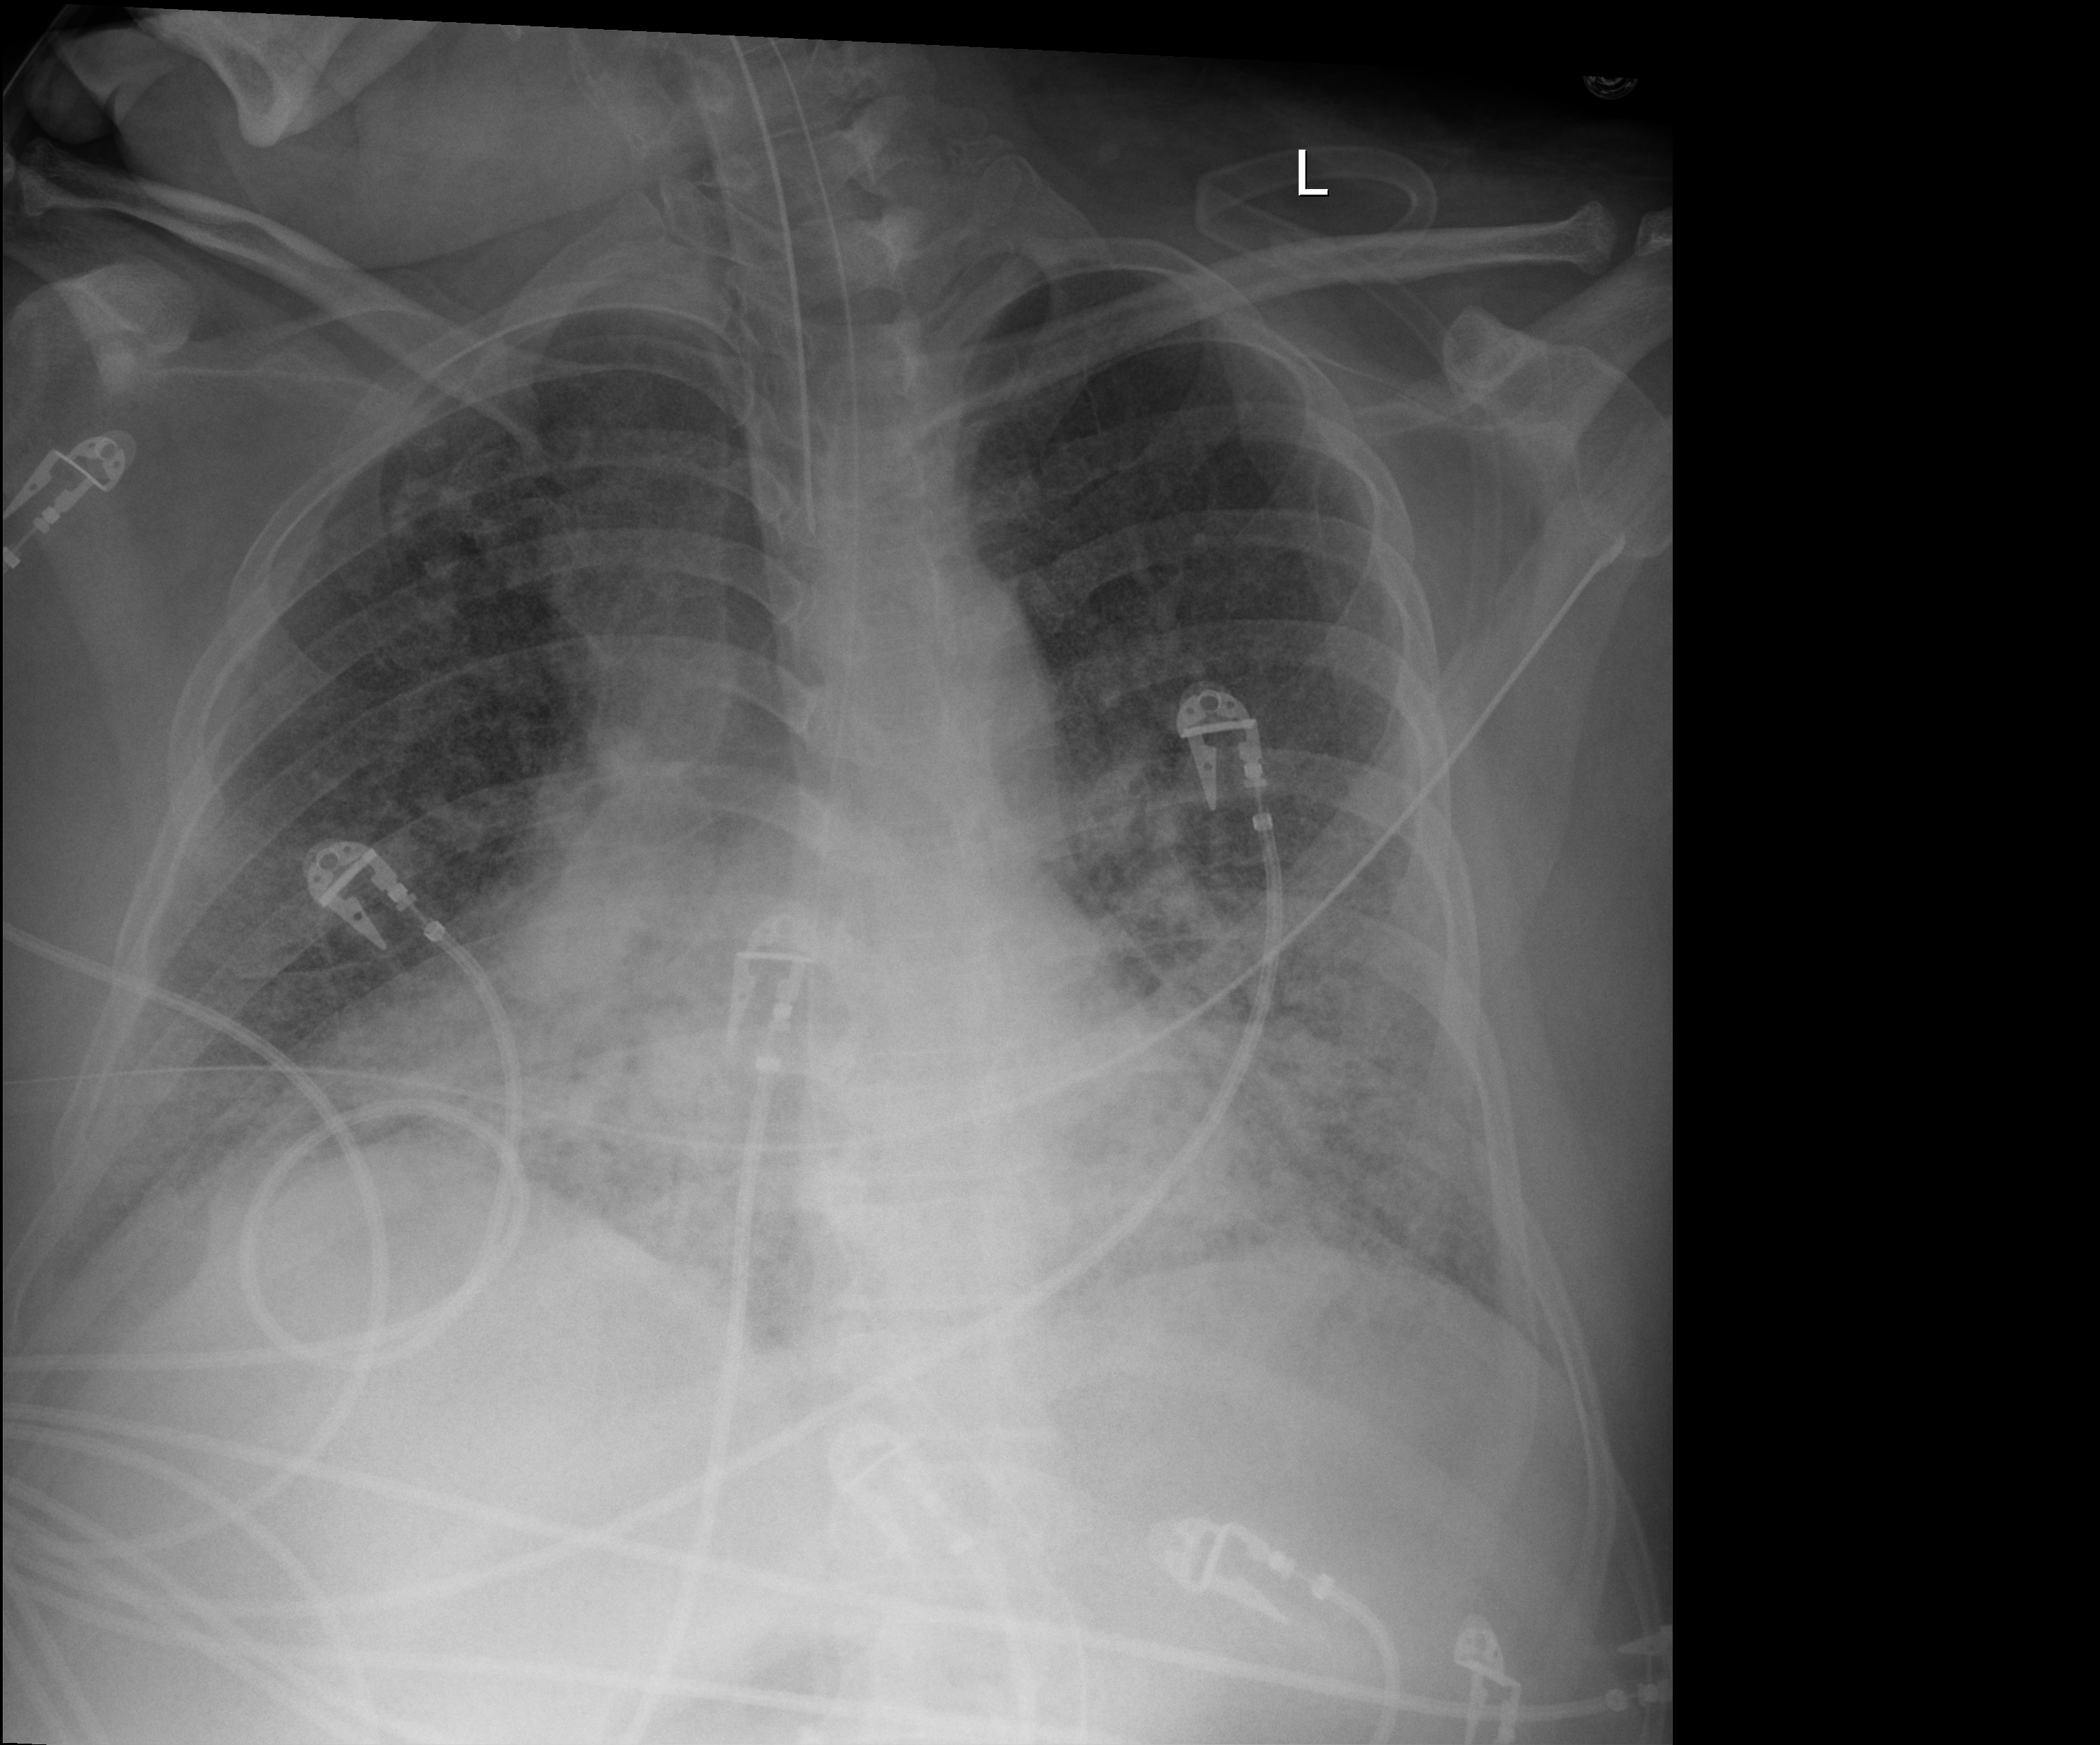
Chest X-ray (portable), anteroposterior (AP) projection. Patient hospitalised with COVID-19, aged 18–59 years.
Admission-level facts for this patient (not findings on this image; timing relative to this image not recorded): hypertension (admission record): no.